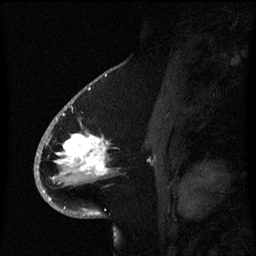
Breast MRI (dynamic contrast-enhanced), one sagittal slice. Position 35 of 60 along the scan axis. Dynamic contrast-enhanced series, image 2 of 3 at this slice position (ordered by acquisition). 1.5 T. TE 4.2 ms, TR 8.4 ms. 256 × 256 image matrix, field of view 200 × 200 mm. Patient: female, 53 years. Case-level facts recorded for this patient, not image findings: setting: breast cancer imaged before/during neoadjuvant chemotherapy; receptor status: HR-positive, HER2-negative.
Structures marked on this image (semi-automatic segmentation, software-assisted and operator-edited):
- analysis volume of interest (the breast-tissue region the enhancement analysis was run in; not a lesion): bounding box (x1, y1, x2, y2) in pixels: (49, 108, 119, 201)
- tumour enhancement mask (voxels above the 70 % enhancement threshold inside the analysis volume of interest): (50, 134, 109, 201)